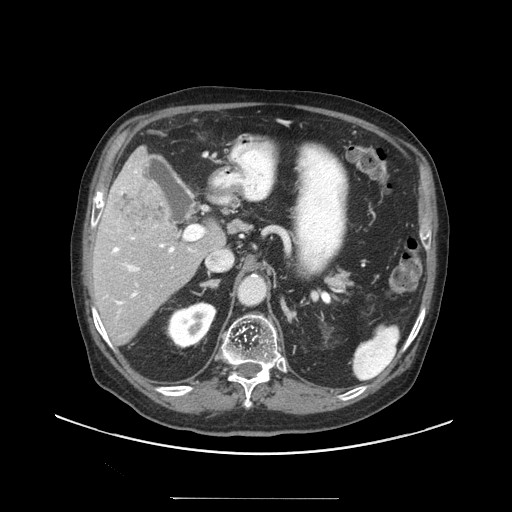
Contrast-enhanced abdominal CT (liver protocol), one axial slice; slice 59 of 97 in the series (ordered by position); soft-tissue window (W 400 / L 40 HU); 512 × 512 image matrix. Case-level facts recorded for this patient, not image findings: diagnosis: hepatocellular carcinoma (patient treated with transarterial chemoembolisation; whether this scan precedes or follows treatment is not stated here); TNM stage (as recorded): Stage-IIIC; Child-Pugh class: A; tumour differentiation: well differentiated; tumour nodularity: uninodular.
Structures marked on this image (semi-automatically segmented with operator editing):
- liver parenchyma outside the tumour (the mass and vessels are separate outlines, so this box may not span the whole liver): bounding box (x1, y1, x2, y2) in pixels: (92, 146, 224, 344)
- mass: (109, 179, 169, 237)
- liver vessels: (112, 169, 194, 305)